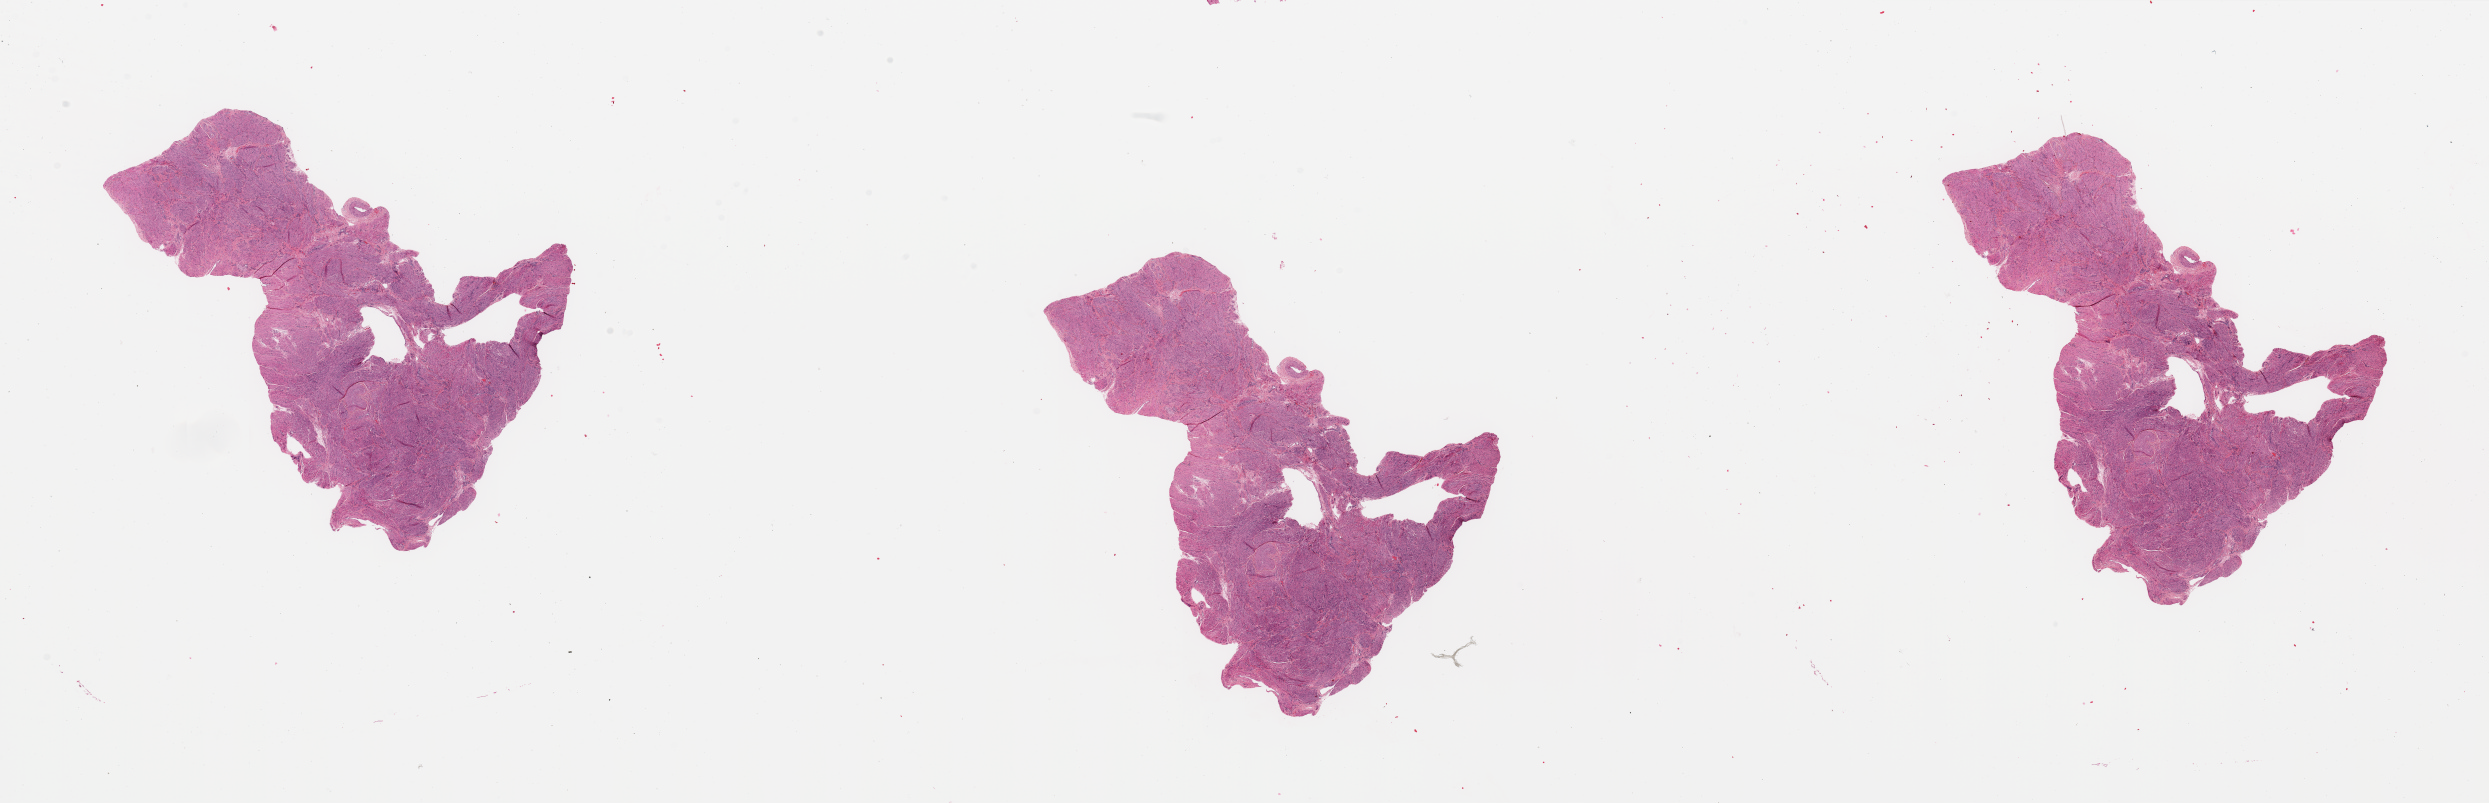
Digitized H&E tissue section (whole slide) — low-resolution overview of the scanned area, about 39.4 x 12.7 mm (acquisition: 20x scan), normal (non-tumour) tissue sample, sampled site: uterus. Patient: female, age 39 years.
- this section: normal (non-tumour) tissue from the same patient
- patient diagnosis: Endometrioid adenocarcinoma, NOS